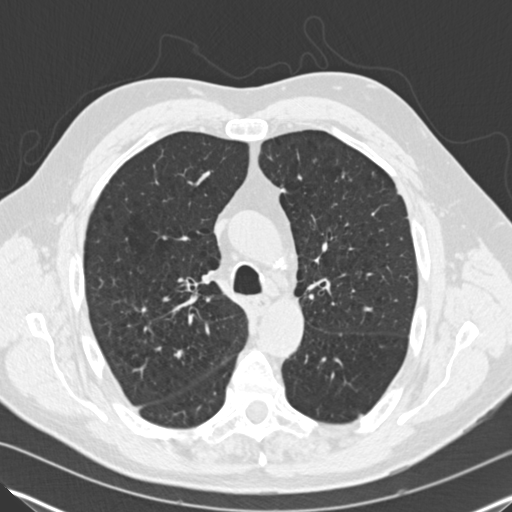
Axial slice from a low-dose chest CT screening exam; baseline annual screen; lung window (W 1500 / L -600 HU); standard (soft-tissue) reconstruction kernel (B30f); slice 56 of 182 in the series. Male participant, aged 65 years at enrolment.
• Expert-annotated lung lesion, bounding box [x1, y1, x2, y2] px = [157, 339, 198, 376].
• The screening reader recorded 5 non-calcified nodules or masses ≥4 mm on this exam (left upper lobe, right upper lobe, right upper lobe, right lower lobe, right upper lobe); which of them this box marks is not recorded.
• Official screen result: positive, change unspecified: nodule(s) >= 4 mm or enlarging nodule(s), mass(es), or other non-specific abnormalities suspicious for lung cancer.